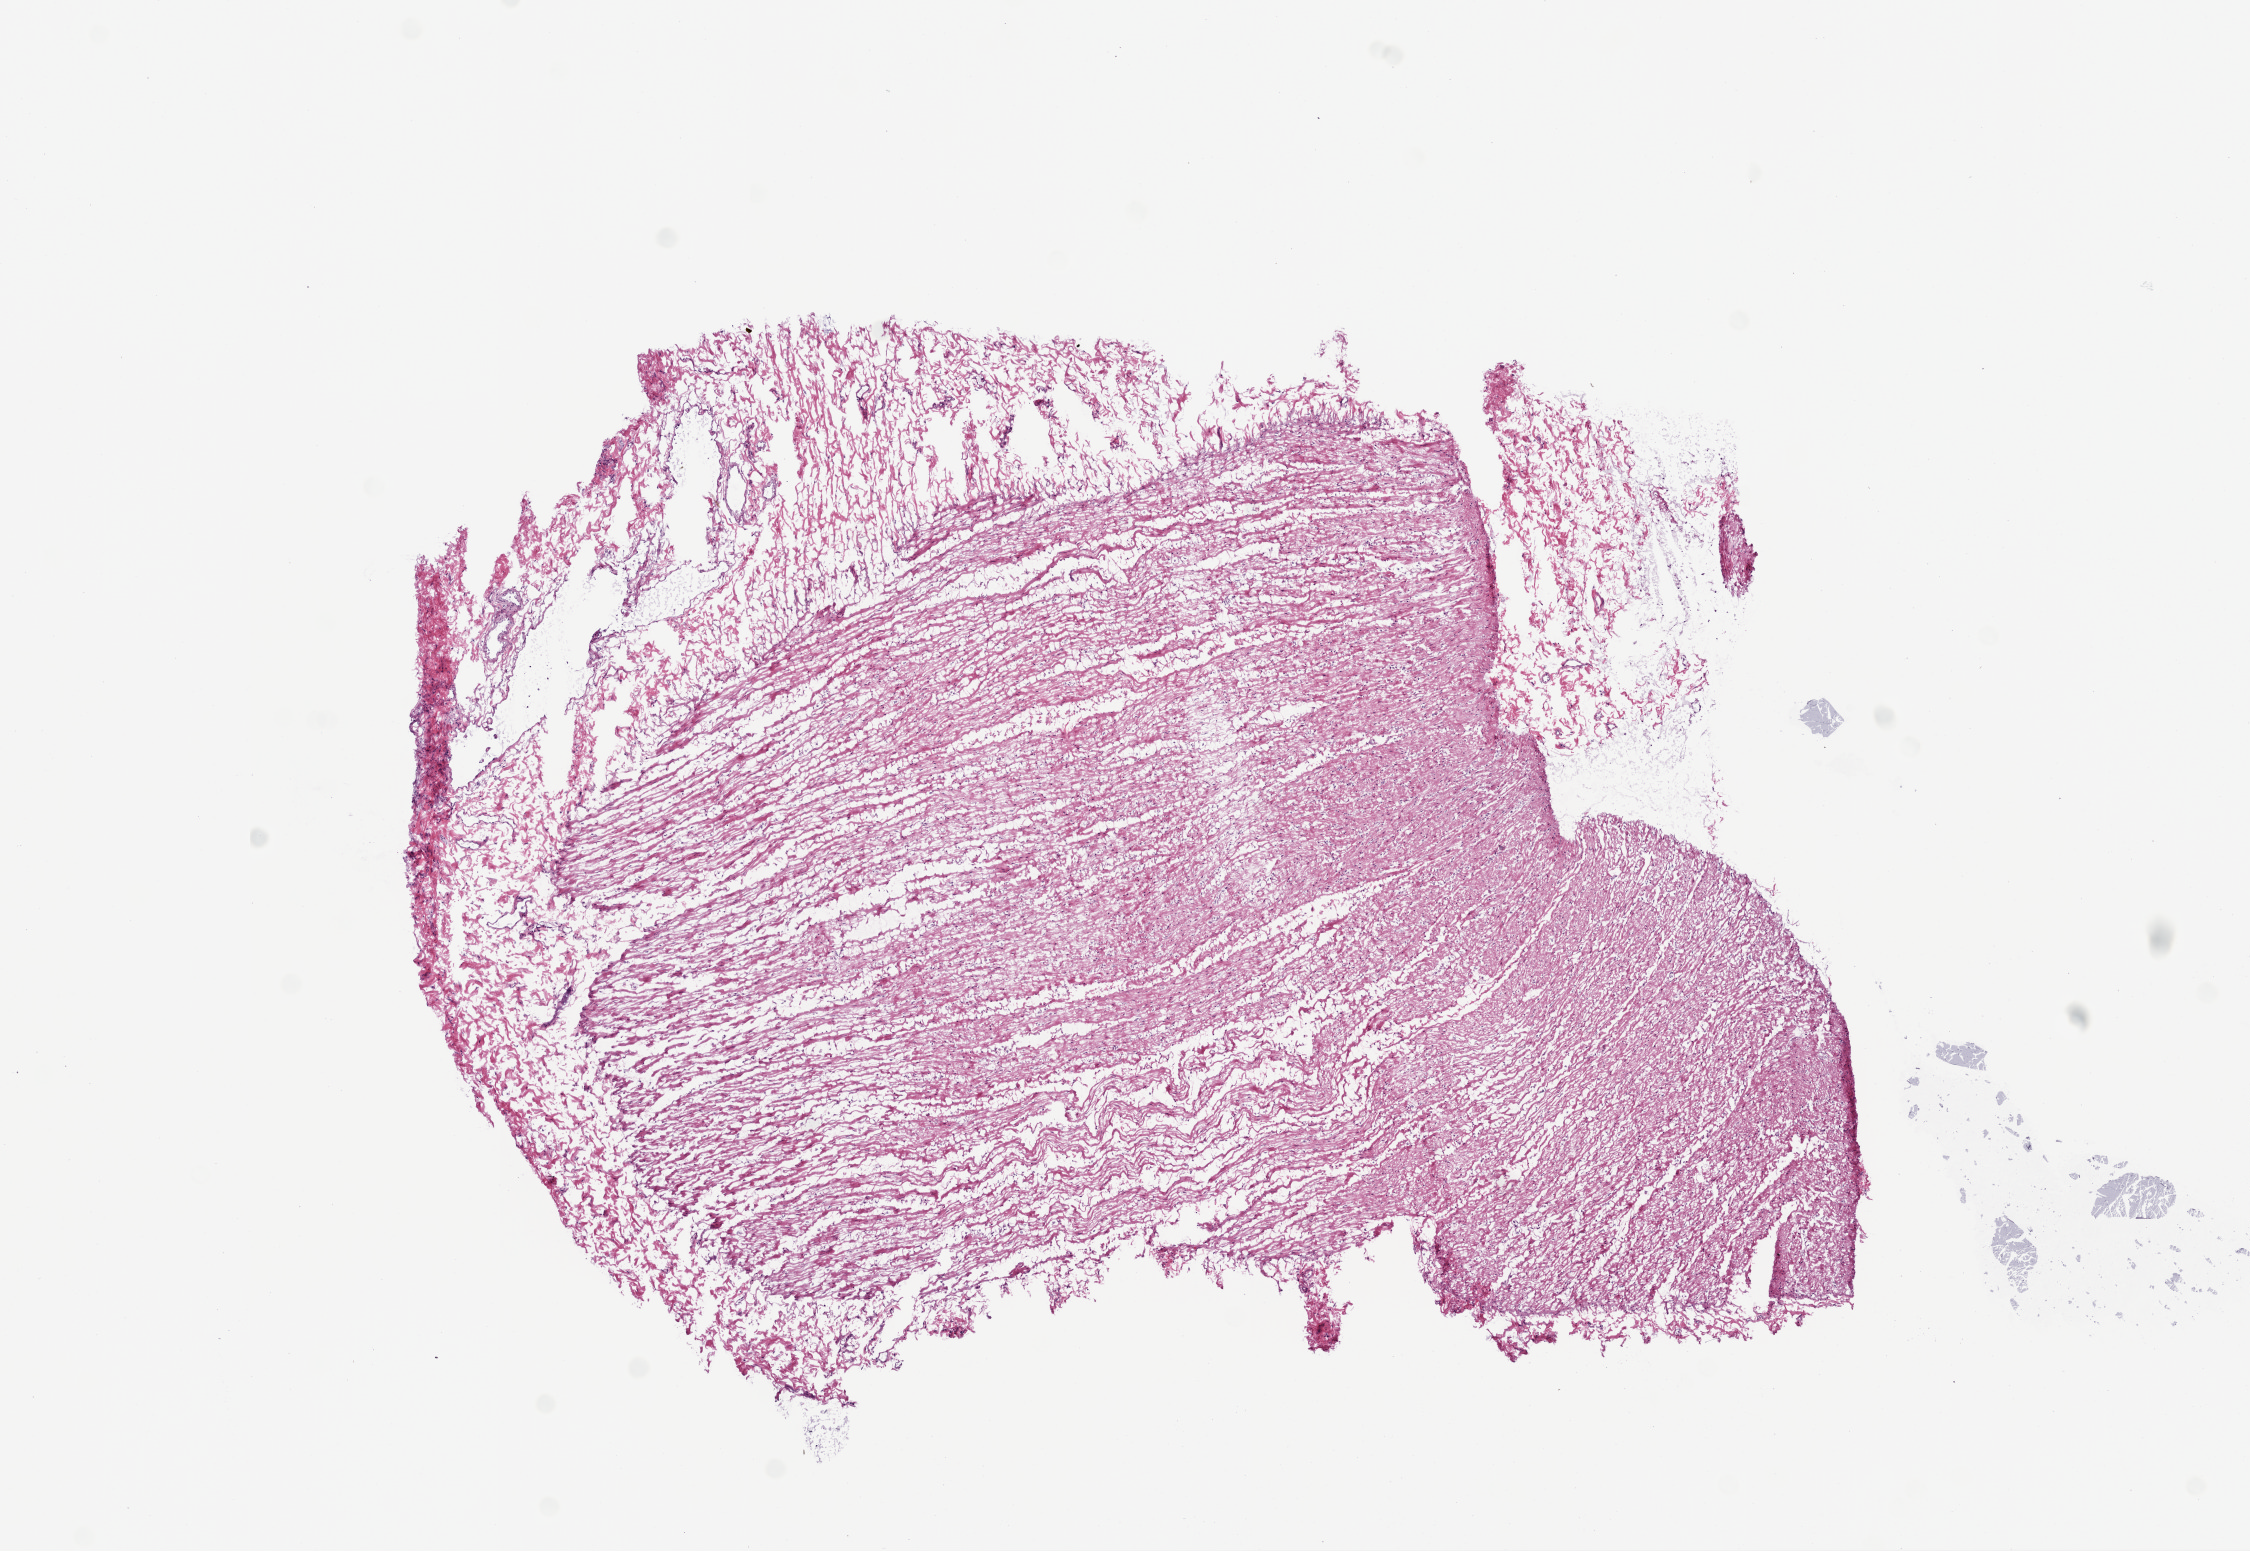
Whole-slide histology image, H&E-stained, a low-resolution overview of the entire scanned area, about 9.0 x 6.2 mm (slide scanned at 20x). Frozen section. Rectum, solid tissue normal (non-tumour tissue) sample. Female patient; age at initial diagnosis 85 years.
* this section: solid tissue normal (non-tumour) sample from the same patient
* patient diagnosis: Adenocarcinoma, NOS (colon, NOS)